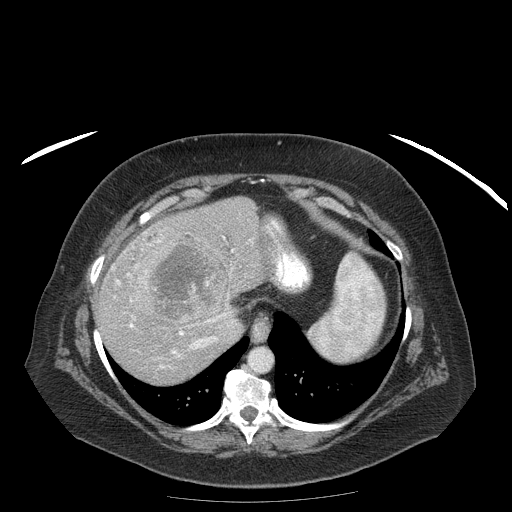
Contrast-enhanced abdominal CT (liver protocol), one axial slice. Position 147 of 204 along the scan axis. Reconstruction kernel STANDARD. 120 kVp. Soft-tissue window (W 400 / L 40 HU). 512 × 512 image matrix, field of view 440 × 440 mm. Case-level facts recorded for this patient, not image findings: diagnosis: hepatocellular carcinoma (patient treated with transarterial chemoembolisation; whether this scan precedes or follows treatment is not stated here); TNM stage (as recorded): Stage-IIIB; Child-Pugh class: A; tumour differentiation: well differentiated; tumour nodularity: uninodular.
Outlined on this slice (semi-automatic segmentation, software-assisted and operator-edited):
- liver parenchyma outside the tumour (the mass and vessels are separate outlines, so this box may not span the whole liver): bounding box <94,196,276,384> (left, top, right, bottom; pixels)
- mass: <134,234,226,330>
- liver vessels: <112,232,253,369>